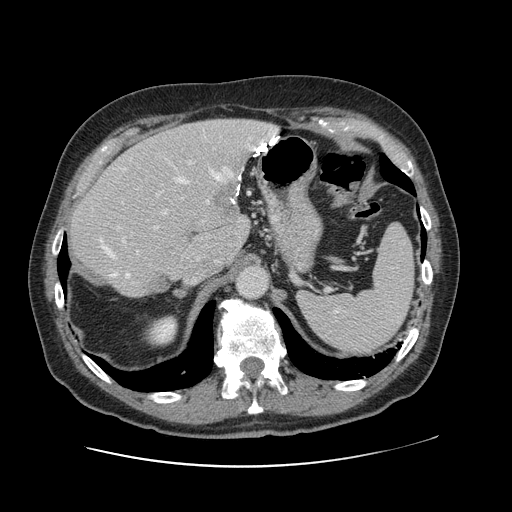
Contrast-enhanced abdominal CT, one axial slice. Slice 81 of 138 in the series (ordered by position). Soft-tissue window (W 400 / L 40 HU). 2.5 mm slice thickness. 512 × 512 image matrix, field of view 402 × 402 mm. Male patient, age 71 years. From the clinical record (not read from this slice): diagnosis: colorectal cancer liver metastases, imaged before liver resection; multiple liver metastases: no; largest metastasis: 3.3 cm; disease in both lobes: no.
Structures marked on this image (manually delineated by an expert):
- hepatic veins: bounding box (x1, y1, x2, y2) in pixels: (100, 139, 265, 278)
- liver: (69, 120, 274, 296)
- planned liver remnant (the part of the liver to remain after resection): (69, 150, 238, 297)
- portal vein (with intrahepatic branches): (121, 161, 196, 243)
- liver metastasis: (211, 183, 239, 215)